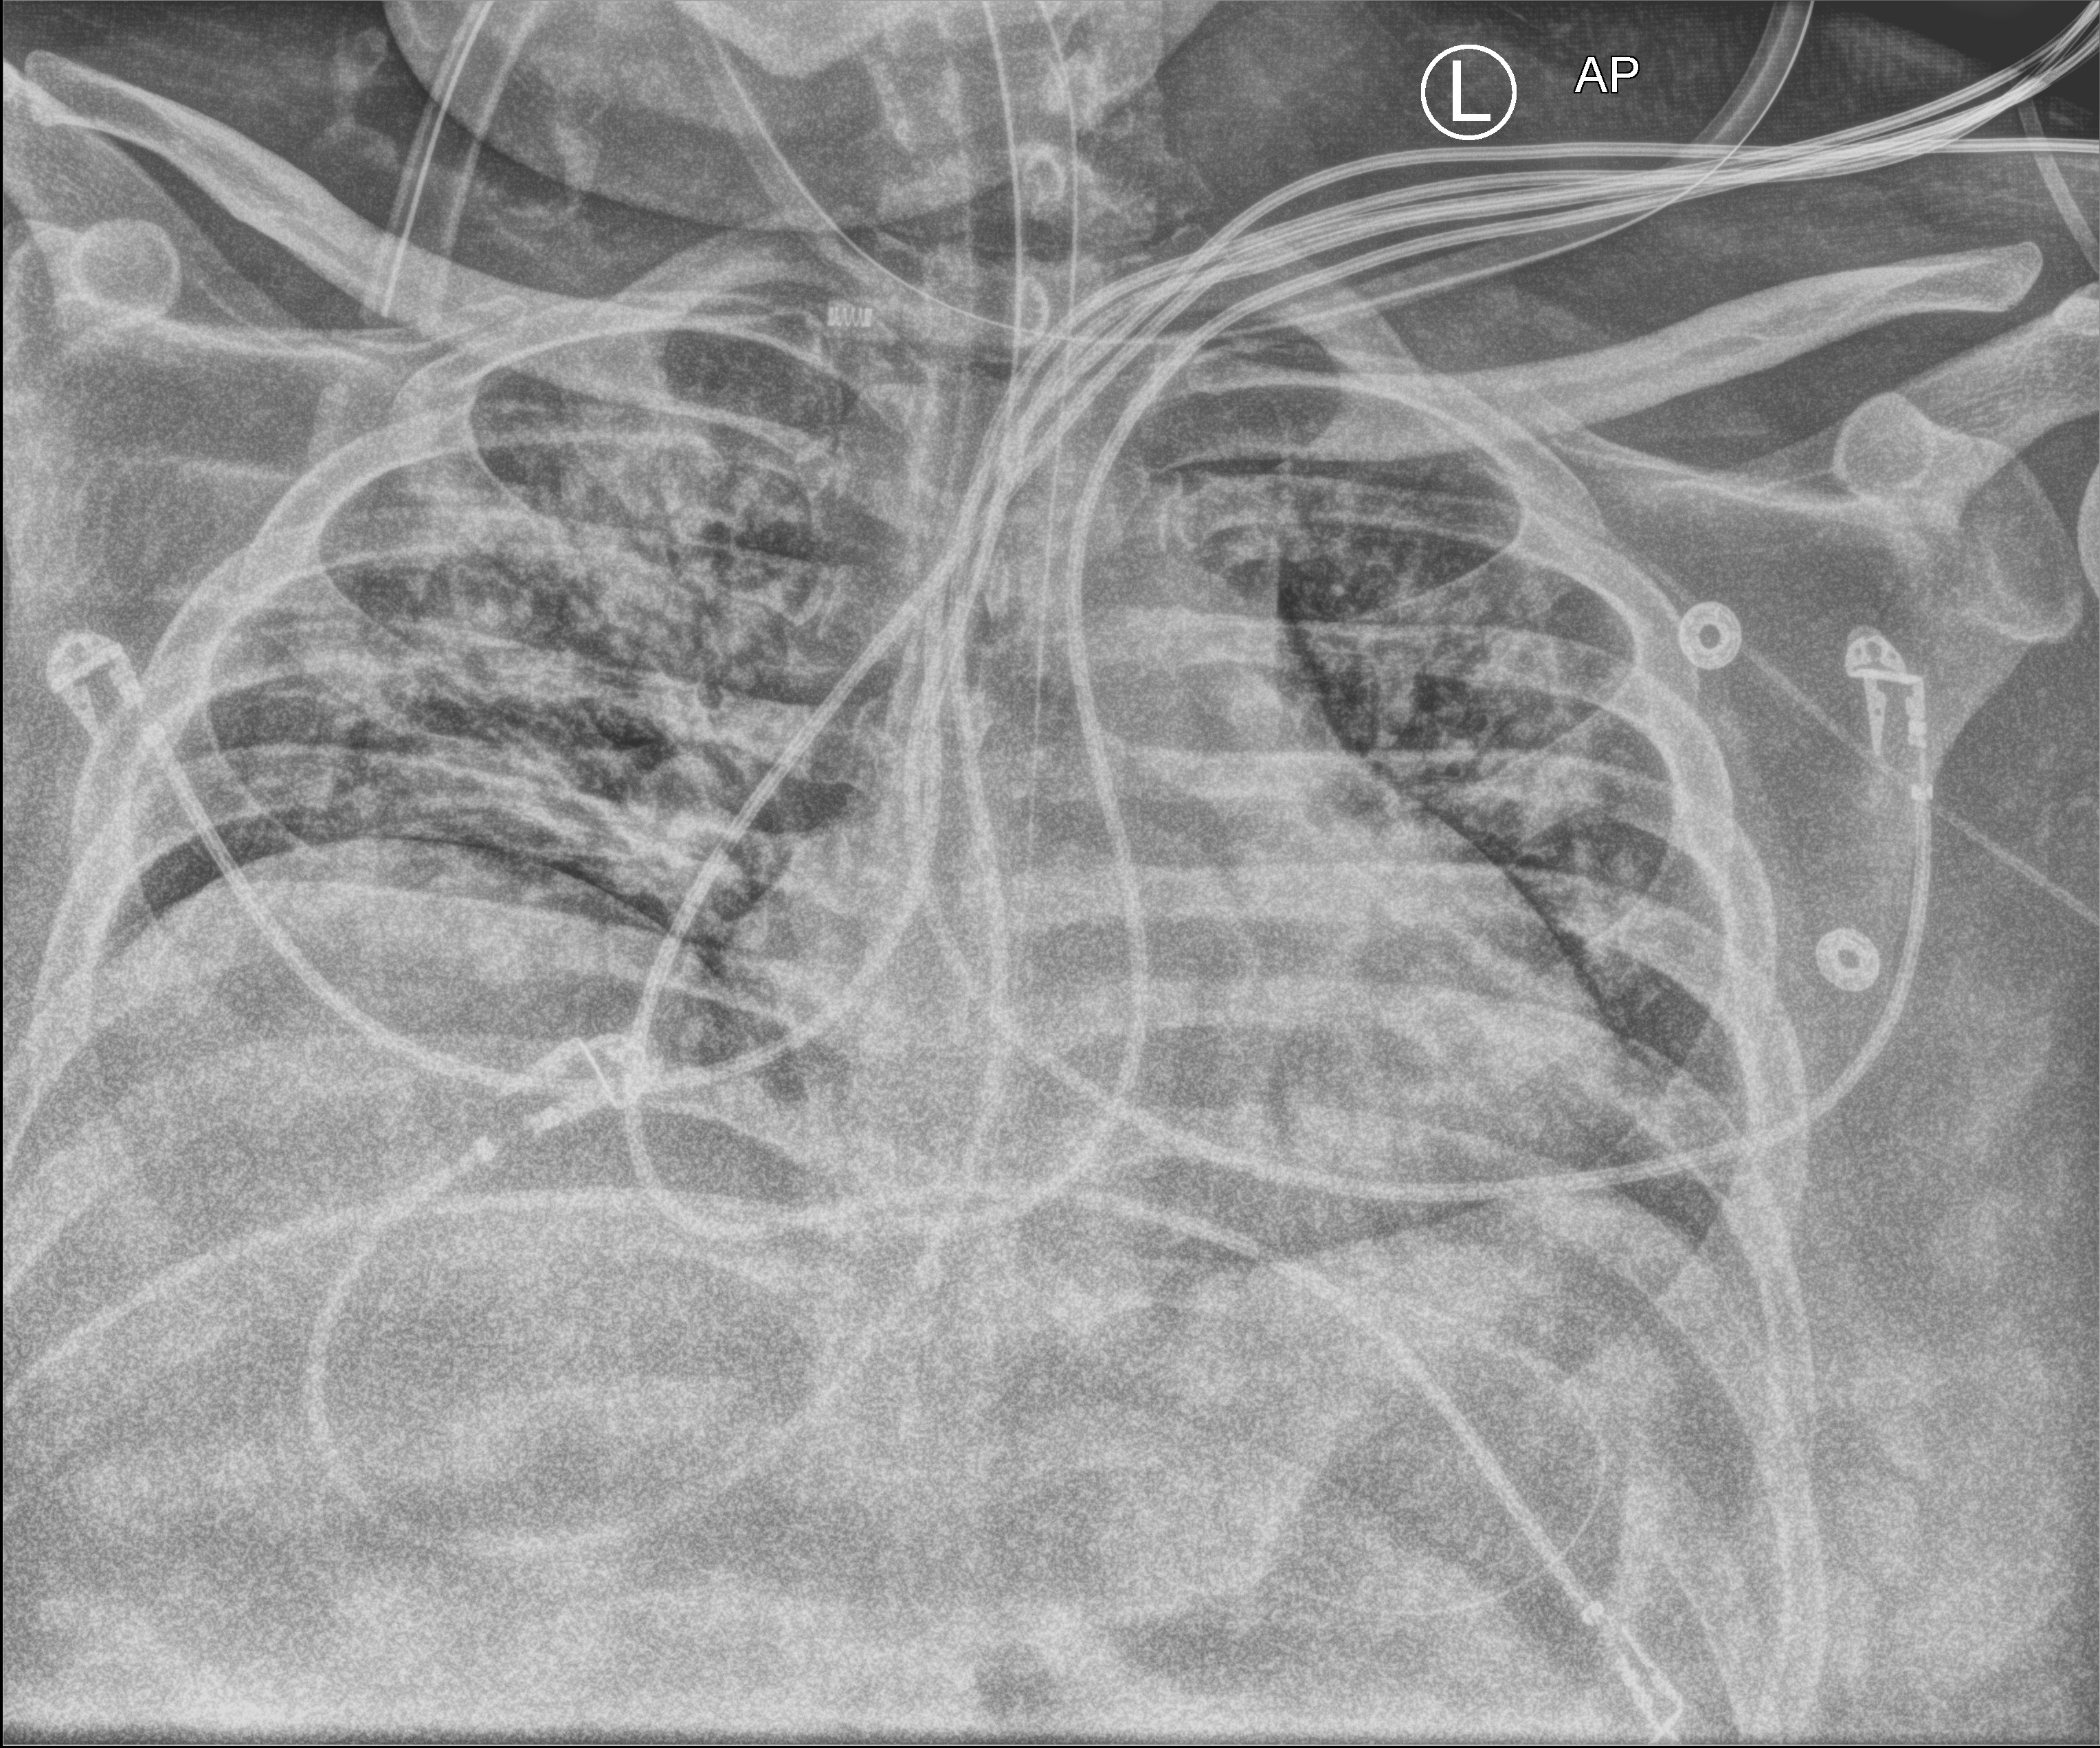
Portable chest radiograph, anteroposterior (AP) projection. Patient hospitalised with COVID-19; male, aged 18–59 years.
Admission-level facts for this patient (not findings on this image; timing relative to this image not recorded): admitted to intensive care during this hospital stay: yes; COPD (admission record): yes.